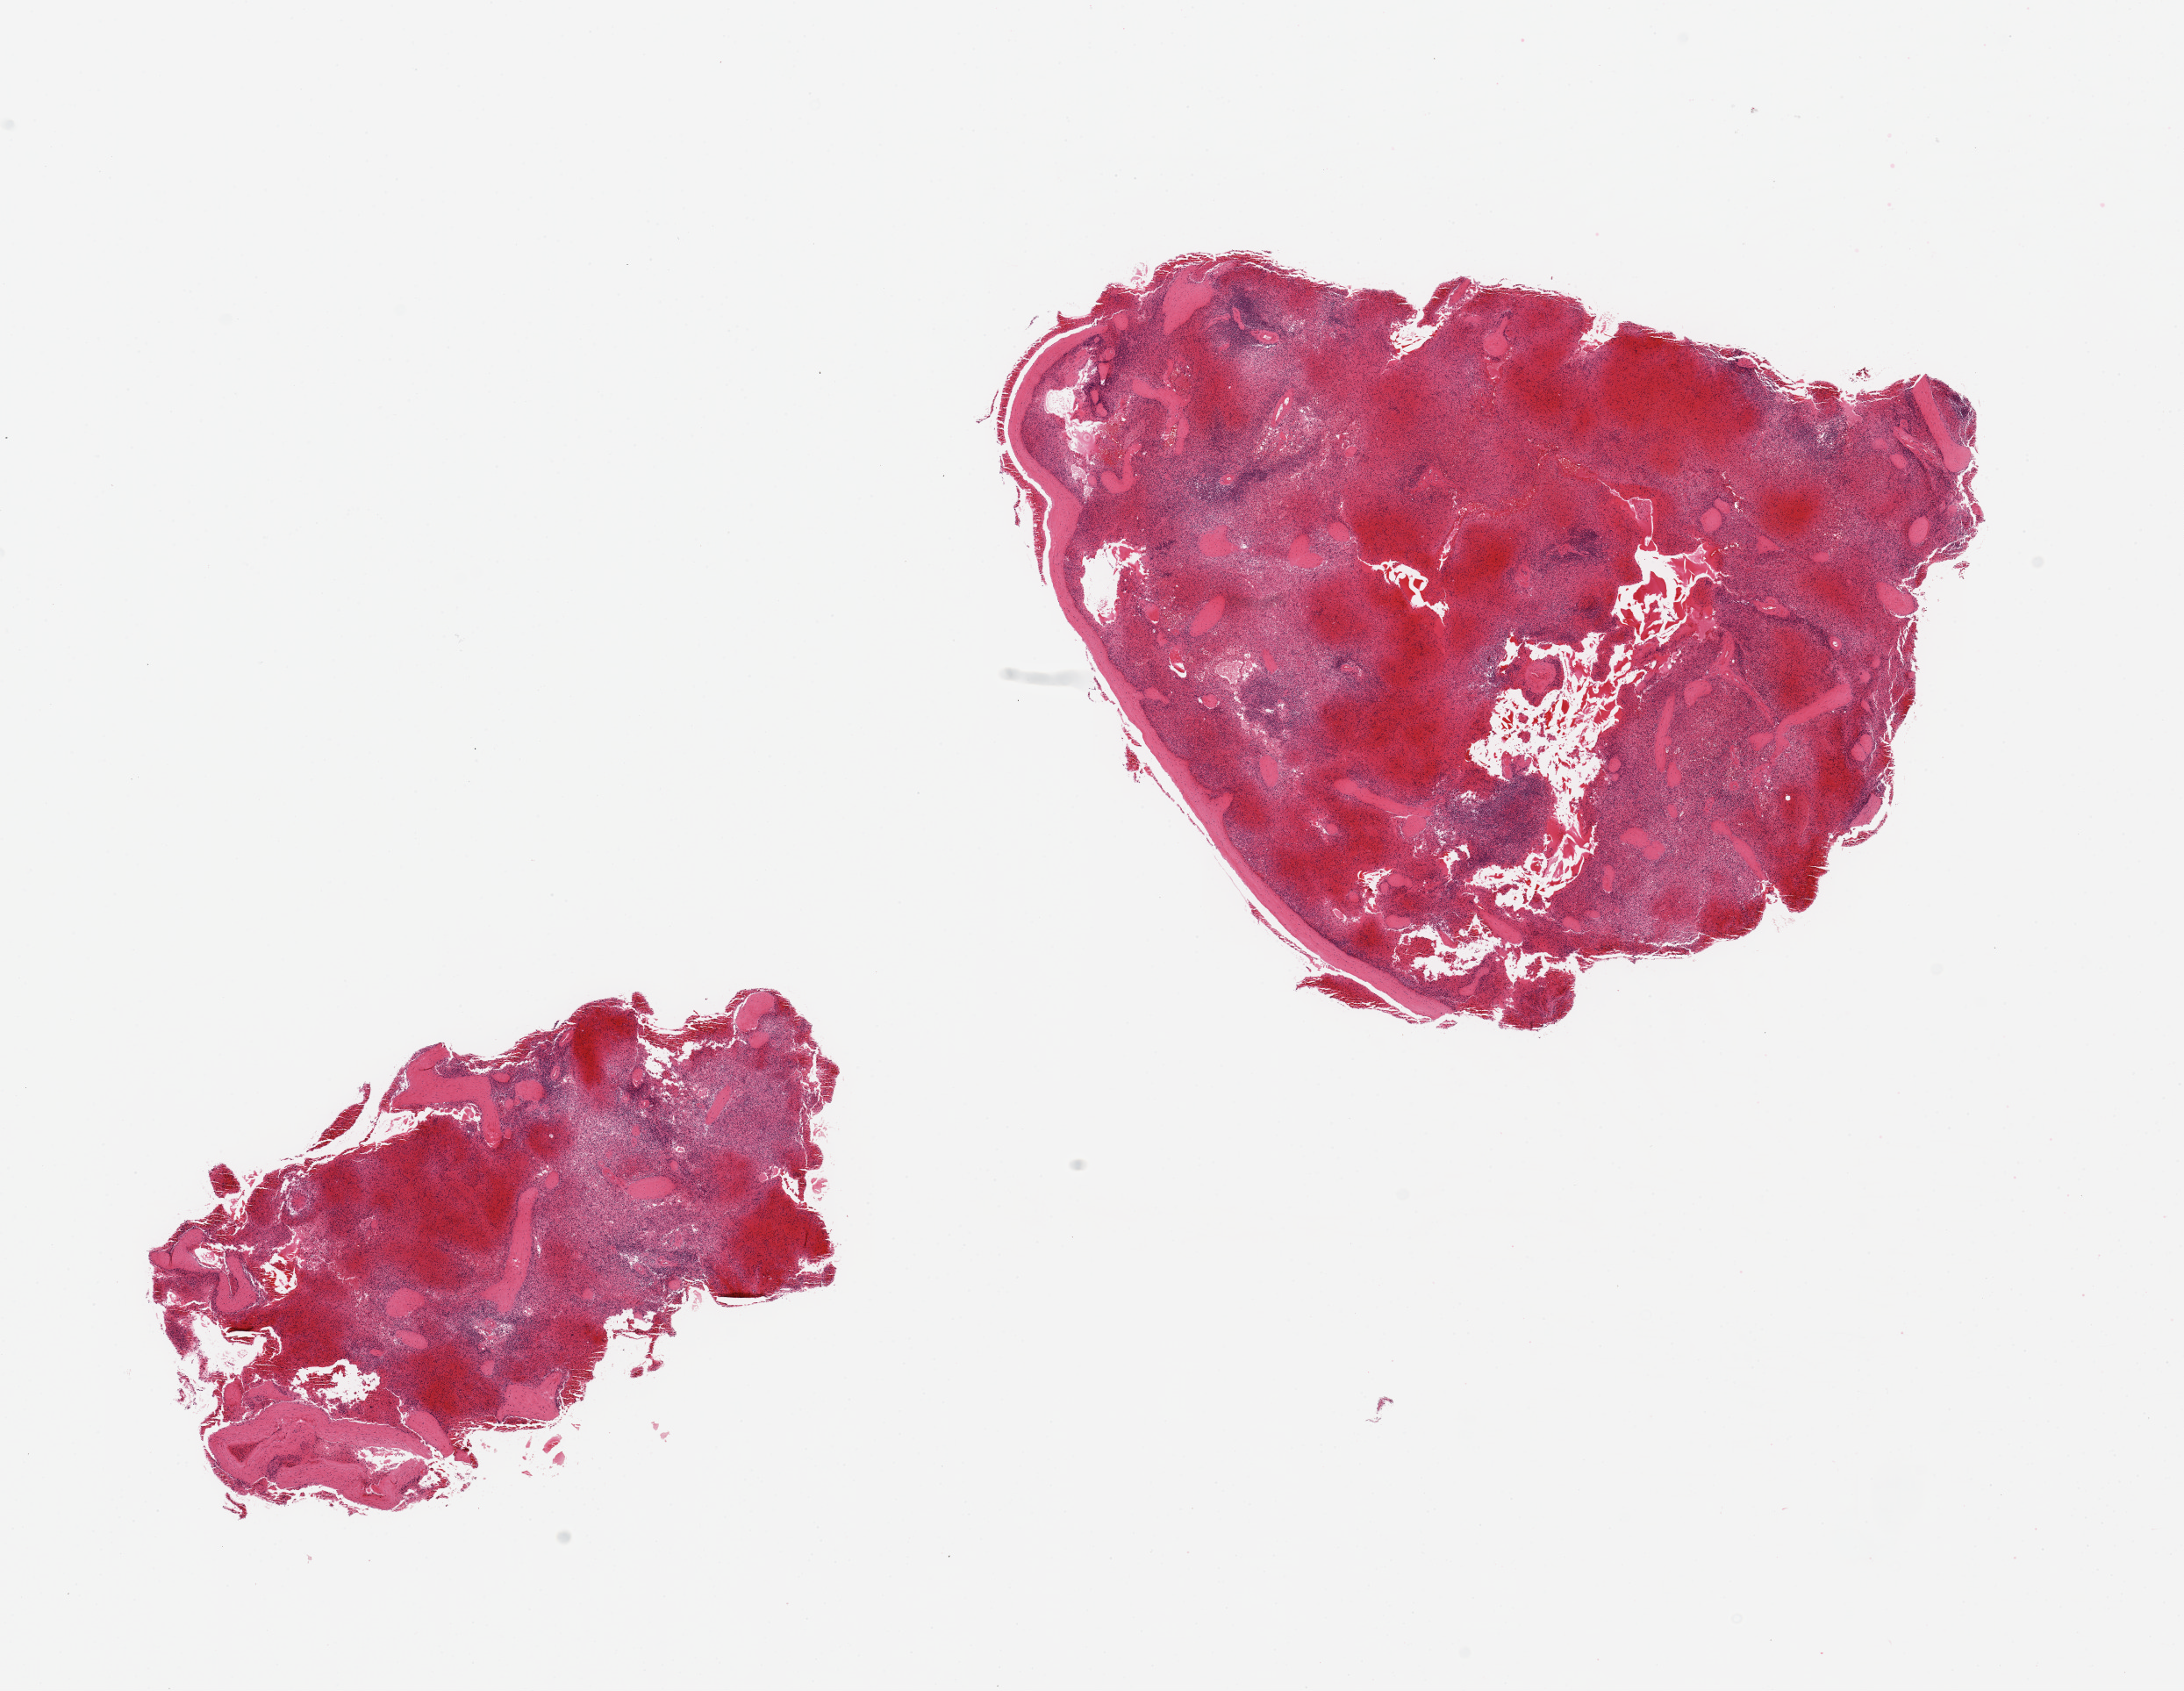
Digitized hematoxylin and eosin (H&E)-stained section, brightfield, shown as a low-resolution overview of the whole scanned area (about 19.7 x 15.2 mm, from a 20x scan); PAXgene-fixed, paraffin-embedded tissue; target tissue: spleen; tissue donor sample.
Reviewer comment on this tissue sample: 2 pieces; congested, includes capsule (target is 5mm below capsule).